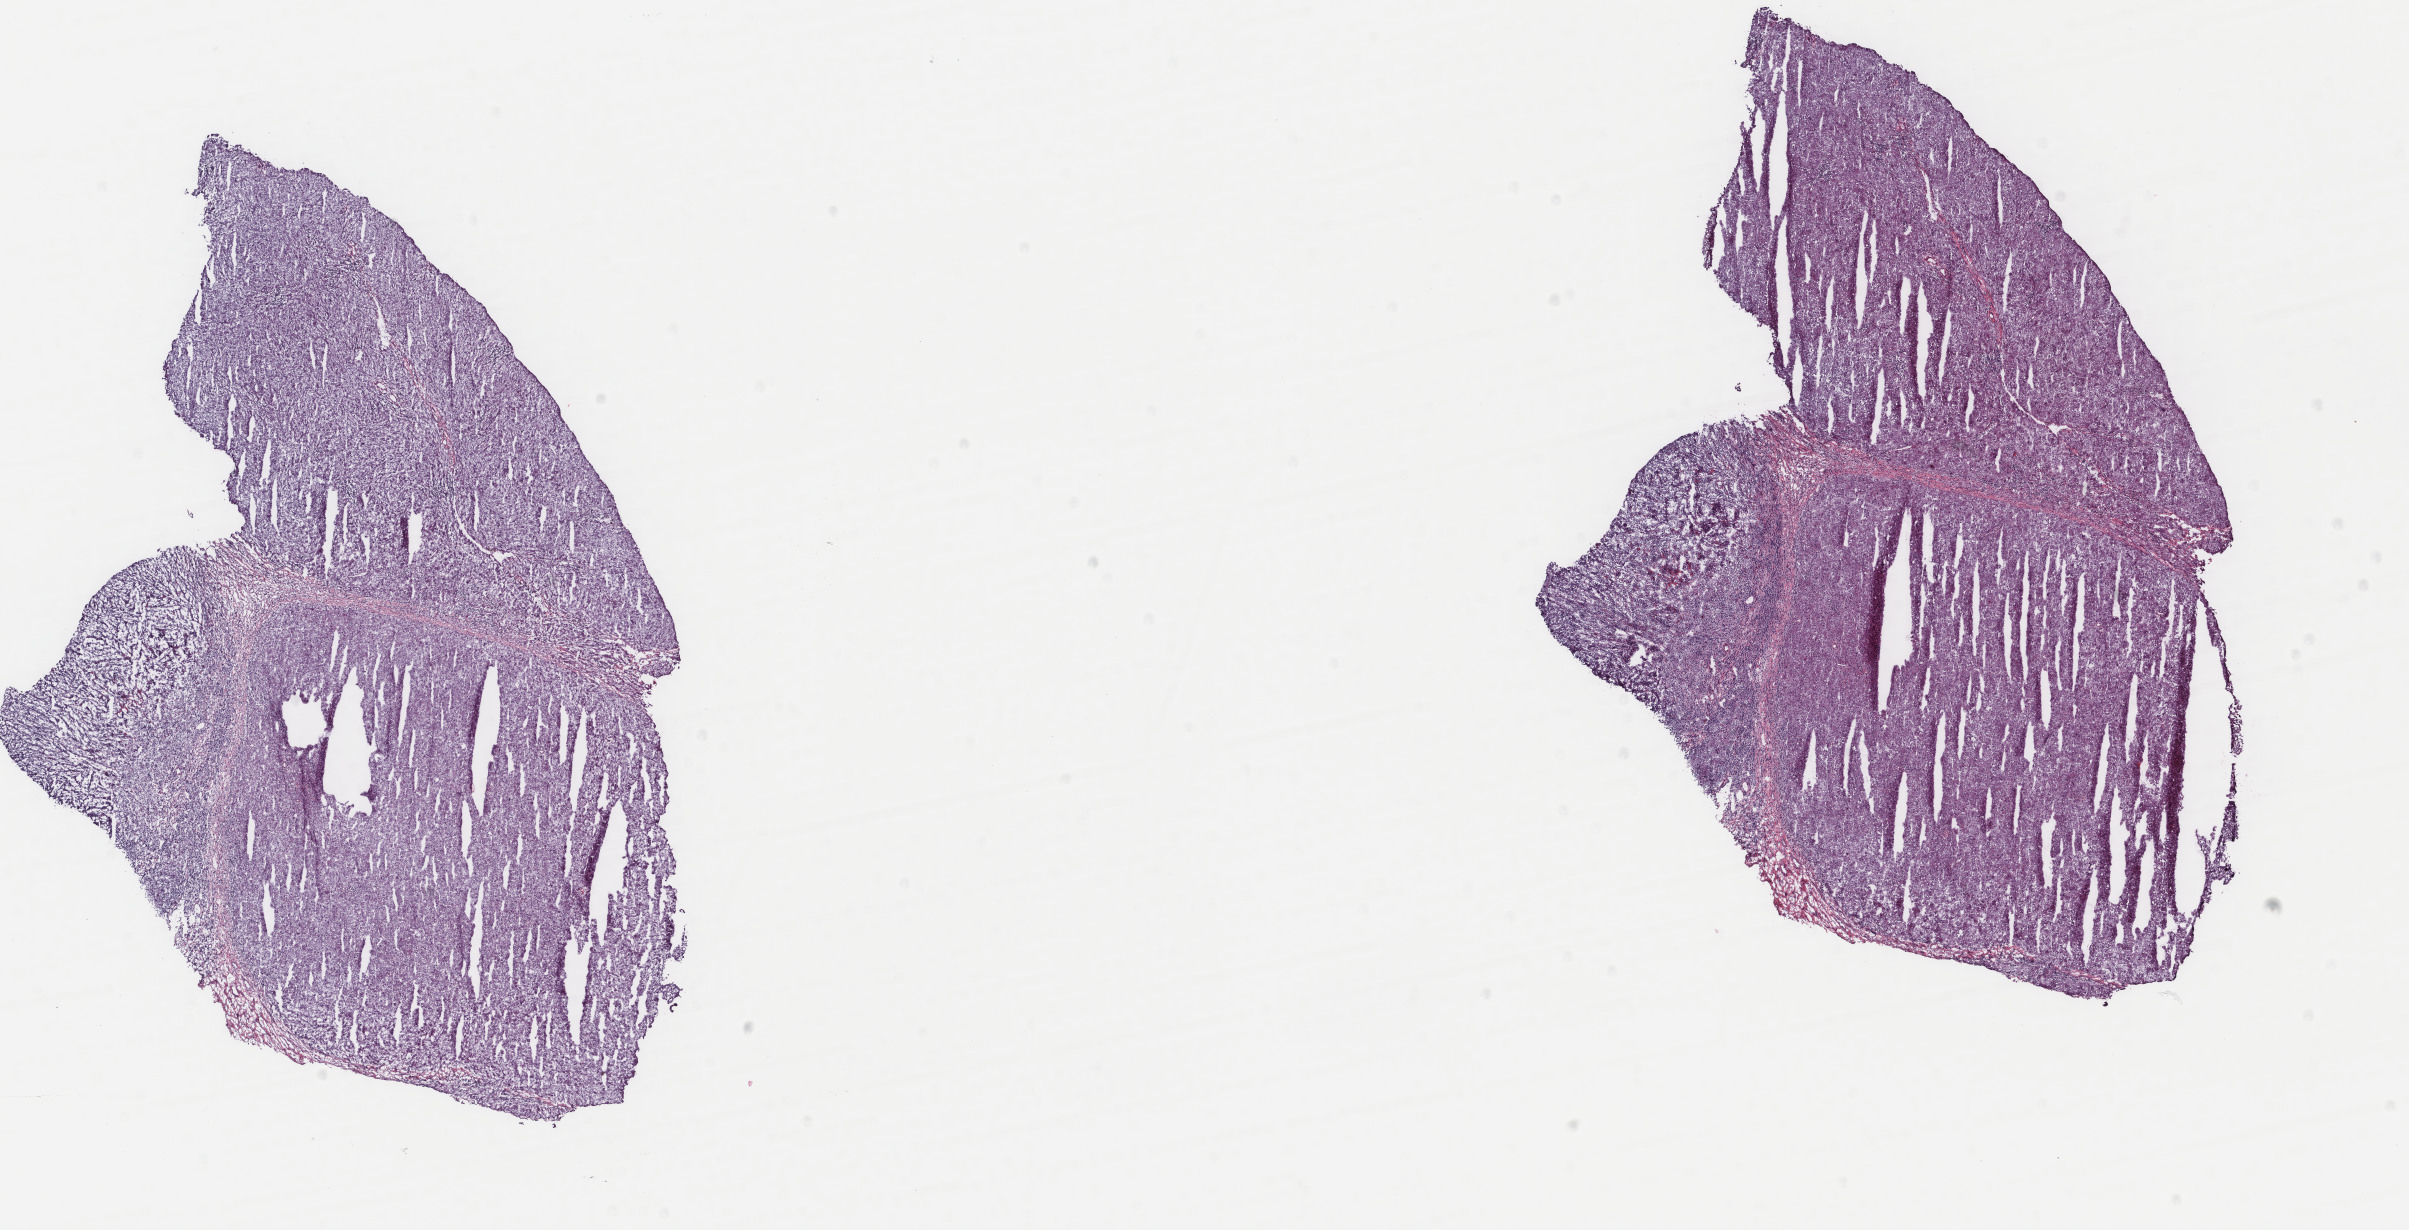
Digitized H&E-stained tissue section (whole slide), shown as a low-resolution overview of the whole scanned area (about 19.1 x 9.8 mm, acquisition: 40x scan), frozen section from the top of the tissue portion, primary tumour sample from the liver. Male patient; age at initial diagnosis 66 years.
Histologic diagnosis: Hepatocellular carcinoma, NOS.